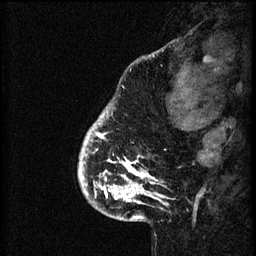
Breast MRI (dynamic contrast-enhanced), one sagittal slice; slice 11 of 60 in the series (ordered by position); 3 images stored at this slice position (order not interpretable as contrast timing); 1.5 T; TE 4.2 ms, TR 8.2 ms; 2 mm slice thickness; 256 × 256 image matrix, field of view 180 × 180 mm. Patient: female, 41 years.
Structures marked on this image (semi-automatic segmentation, software-assisted and operator-edited):
- analysis volume of interest (the breast-tissue region the enhancement analysis was run in; not a lesion): box from (x=79, y=108) to (x=174, y=205) px
- tumour enhancement mask (voxels above the 70 % enhancement threshold inside the analysis volume of interest): (x=79, y=114)–(x=166, y=205)